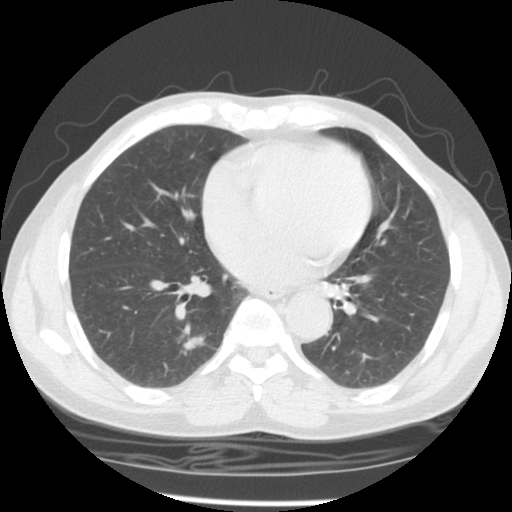
Low-dose screening chest CT, one axial slice; position 57 of 127 along the scan axis; reconstruction kernel STANDARD; 140 kVp; lung window (W 1500 / L -600 HU); 2.5 mm slice thickness; 512 × 512 image matrix, field of view 320 × 320 mm.
Outlined on this slice (expert manual segmentation):
- lesion 1 (tumor, lower lobe of right lung): bounding box <183,336,204,350> (left, top, right, bottom; pixels)